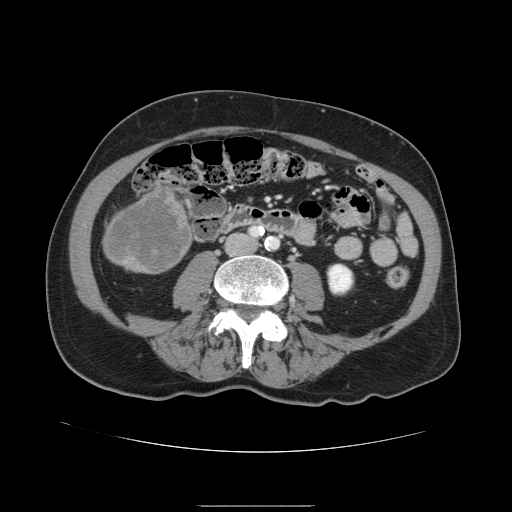
Contrast-enhanced abdominal CT, one axial slice; position 21 of 168 along the scan axis; 120 kVp; intravenous contrast given; soft-tissue window (W 400 / L 40 HU); 512 × 512 image matrix. Male patient, age 74 years. From the clinical record (not read from this slice): diagnosis: colorectal cancer liver metastases, imaged before liver resection; multiple liver metastases: no; largest metastasis: 14.5 cm; disease in both lobes: yes.
Structures marked on this image (manually delineated by an expert):
- liver: bounding box (x1, y1, x2, y2) in pixels: (104, 185, 193, 274)
- liver metastasis: (108, 189, 190, 272)